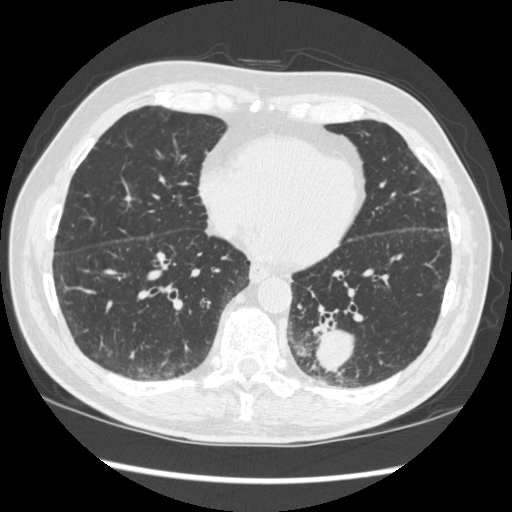
Low-dose screening chest CT, one axial slice; slice 118 of 348 in the series (ordered by position); reconstruction kernel STANDARD; 120 kVp; lung window (W 1500 / L -600 HU); 1.25 mm slice thickness; 512 × 512 image matrix.
Outlined on this slice (manually delineated by an expert):
- lesion 1 (tumor, lower lobe of left lung): box from (x=315, y=330) to (x=354, y=373) px